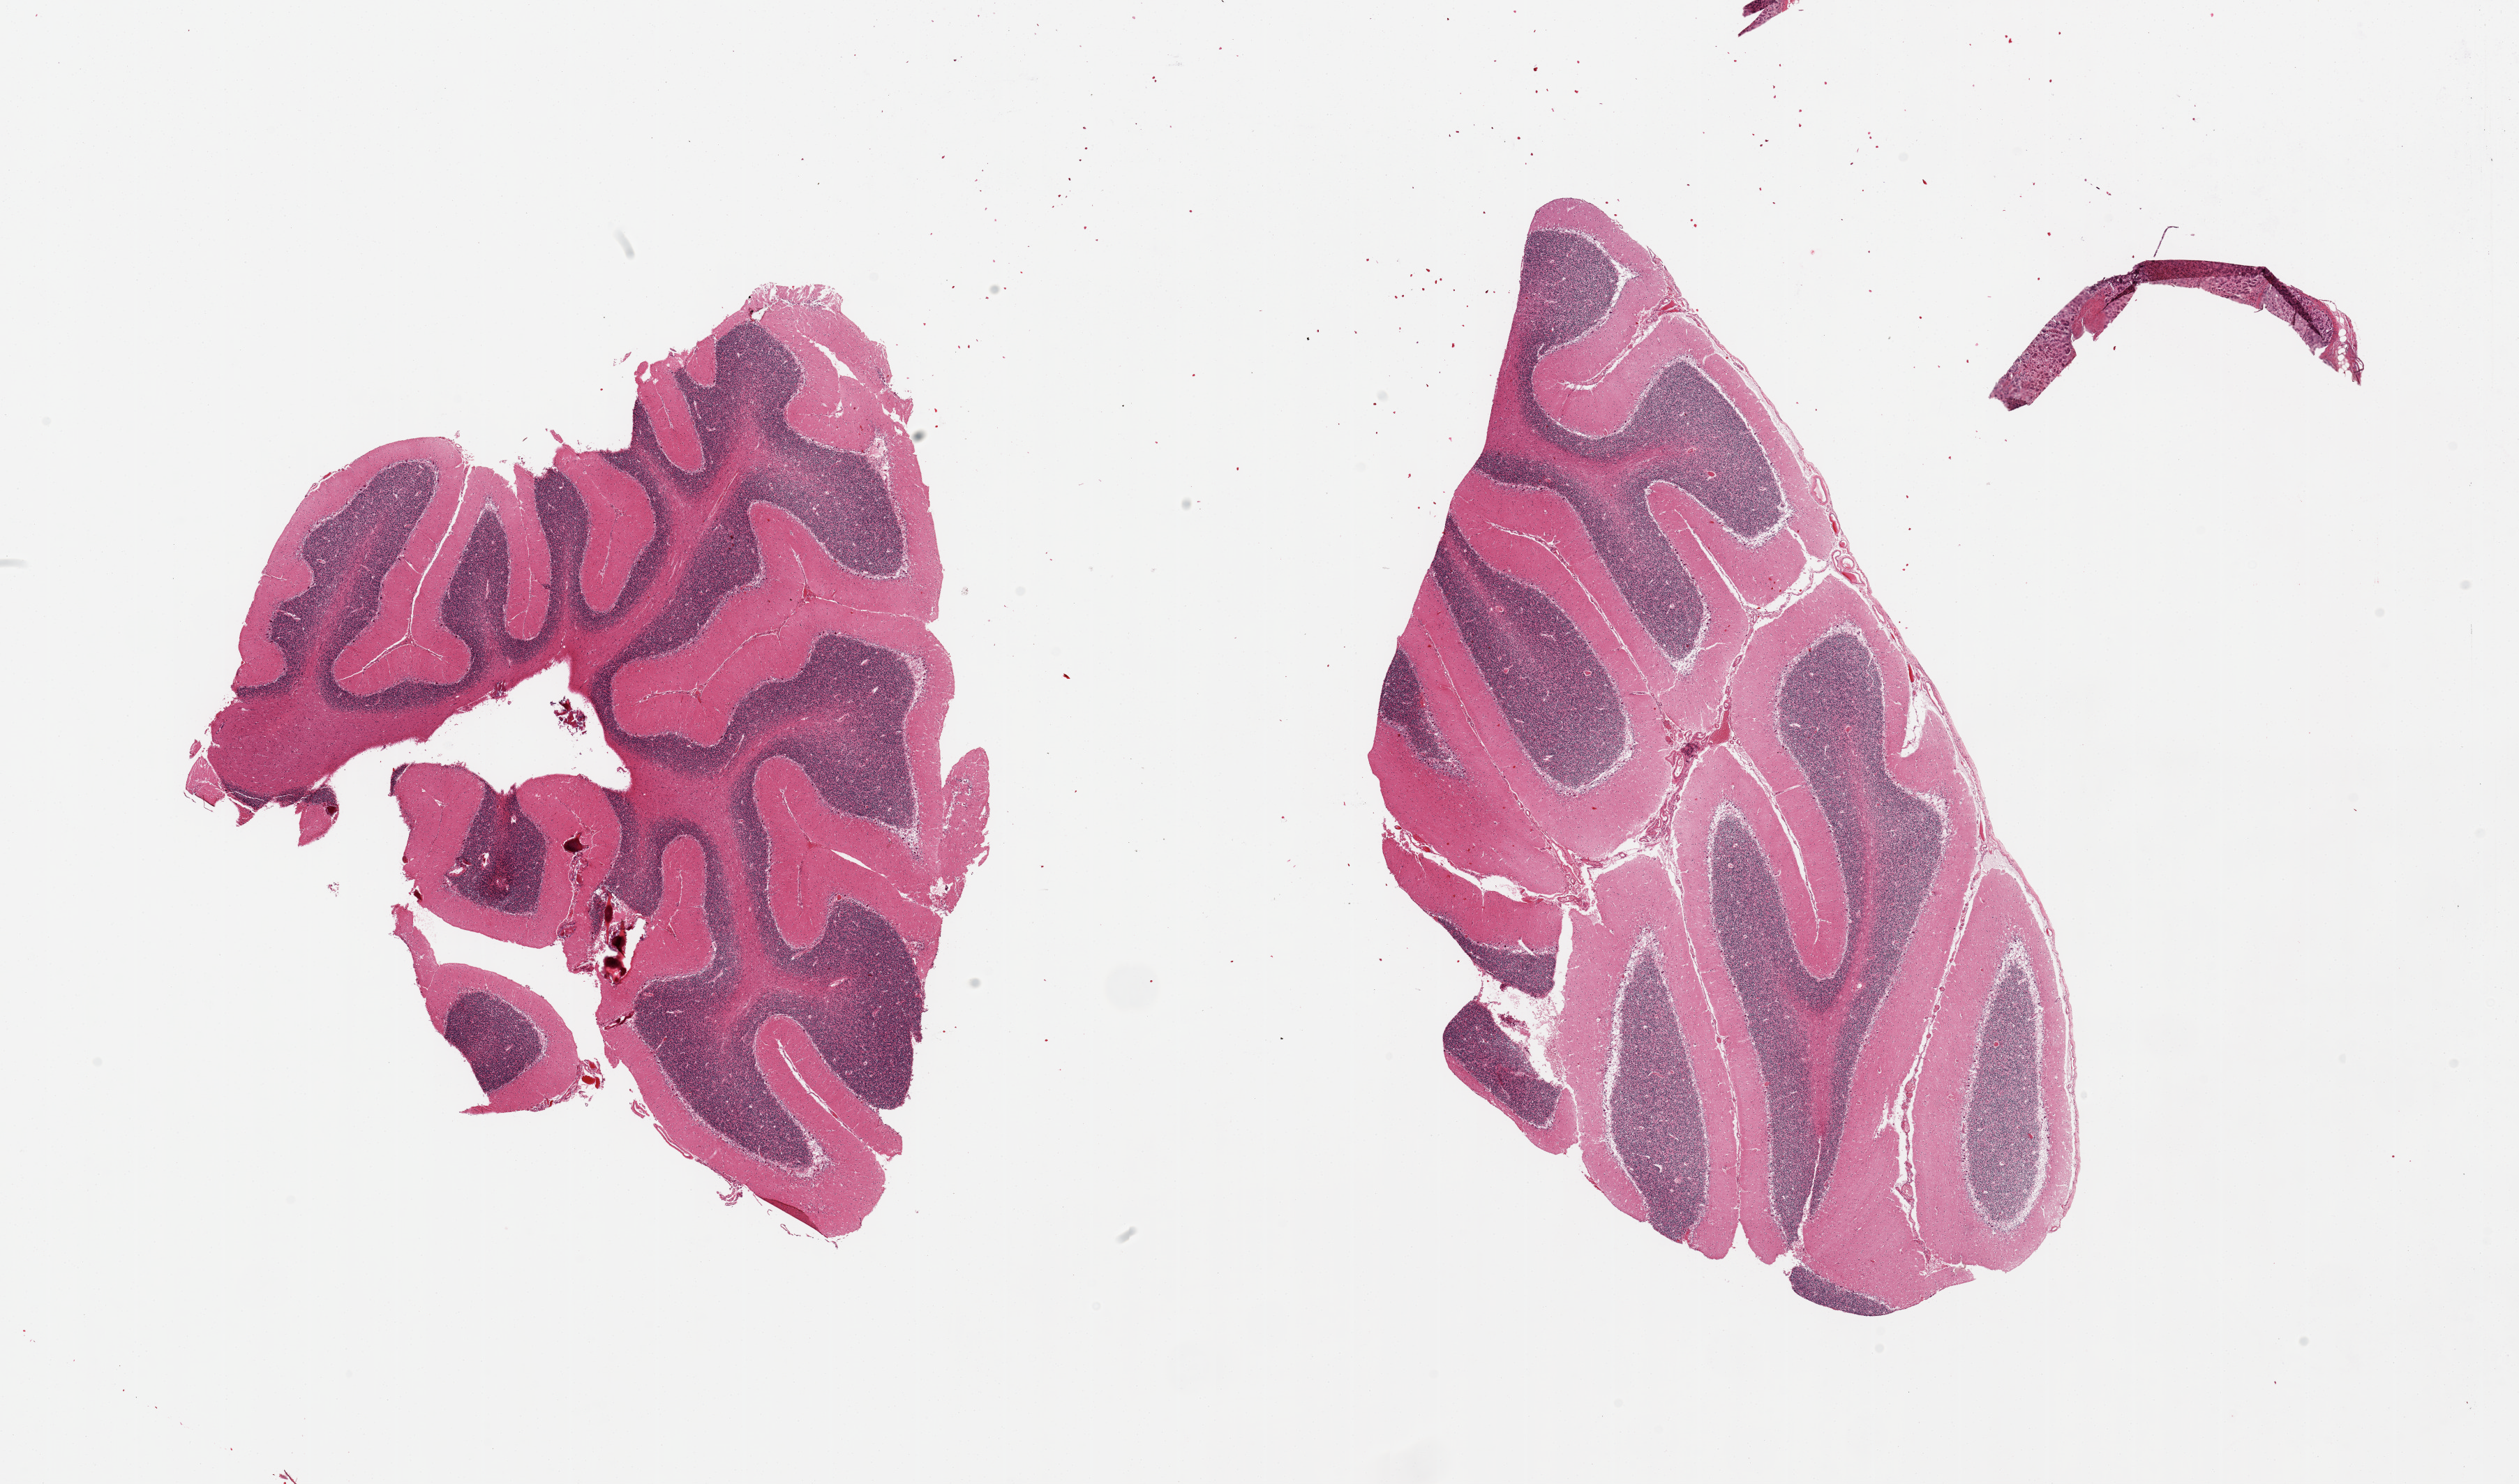
Whole-slide image, haematoxylin and eosin stain — a low-resolution overview of the entire scanned area, about 28.5 x 16.8 mm, PAXgene-fixed, paraffin-embedded tissue, sampled site (target tissue): cerebellum, tissue donor sample. Donor sex: female.
Review note (as recorded): 2 pieces; some Purkinje cells with changes suggestive of hypoxic damage.